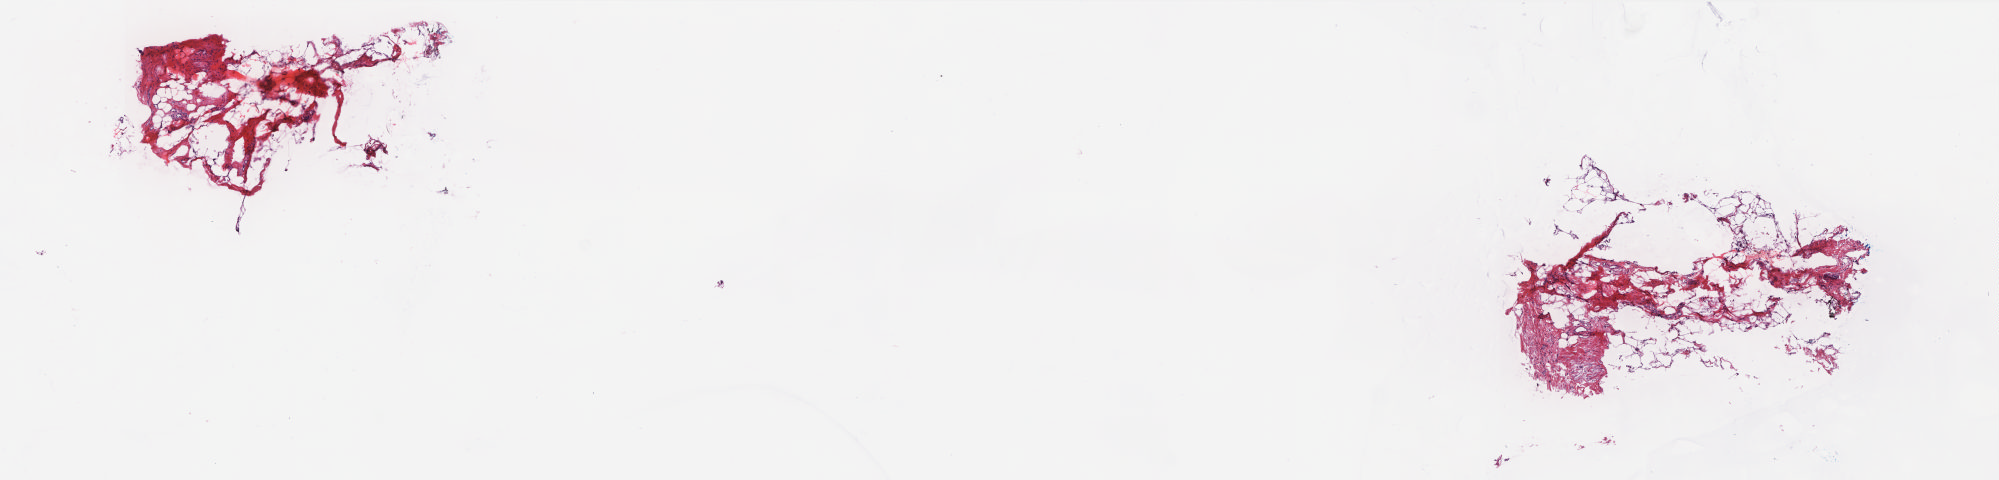
Whole-slide histology image, Hematoxylin and eosin (H&E) stained, shown as a low-resolution overview of the whole scanned area (about 16.0 x 3.8 mm, slide scanned at 20x), frozen section, solid tissue normal (non-tumour tissue) sample from the breast. Patient: female, age at initial diagnosis 65 years. Pathologist review of this section (percent, as recorded): tumour cells 0%, tumour nuclei 0%, normal cells 100%, stromal cells 0%, necrosis 0%. Infiltration values recorded for this section: lymphocyte infiltration 0%, monocyte infiltration 0%, neutrophil infiltration 0%.
- this section: solid tissue normal (non-tumour) sample from the same patient
- patient diagnosis: Lobular carcinoma, NOS